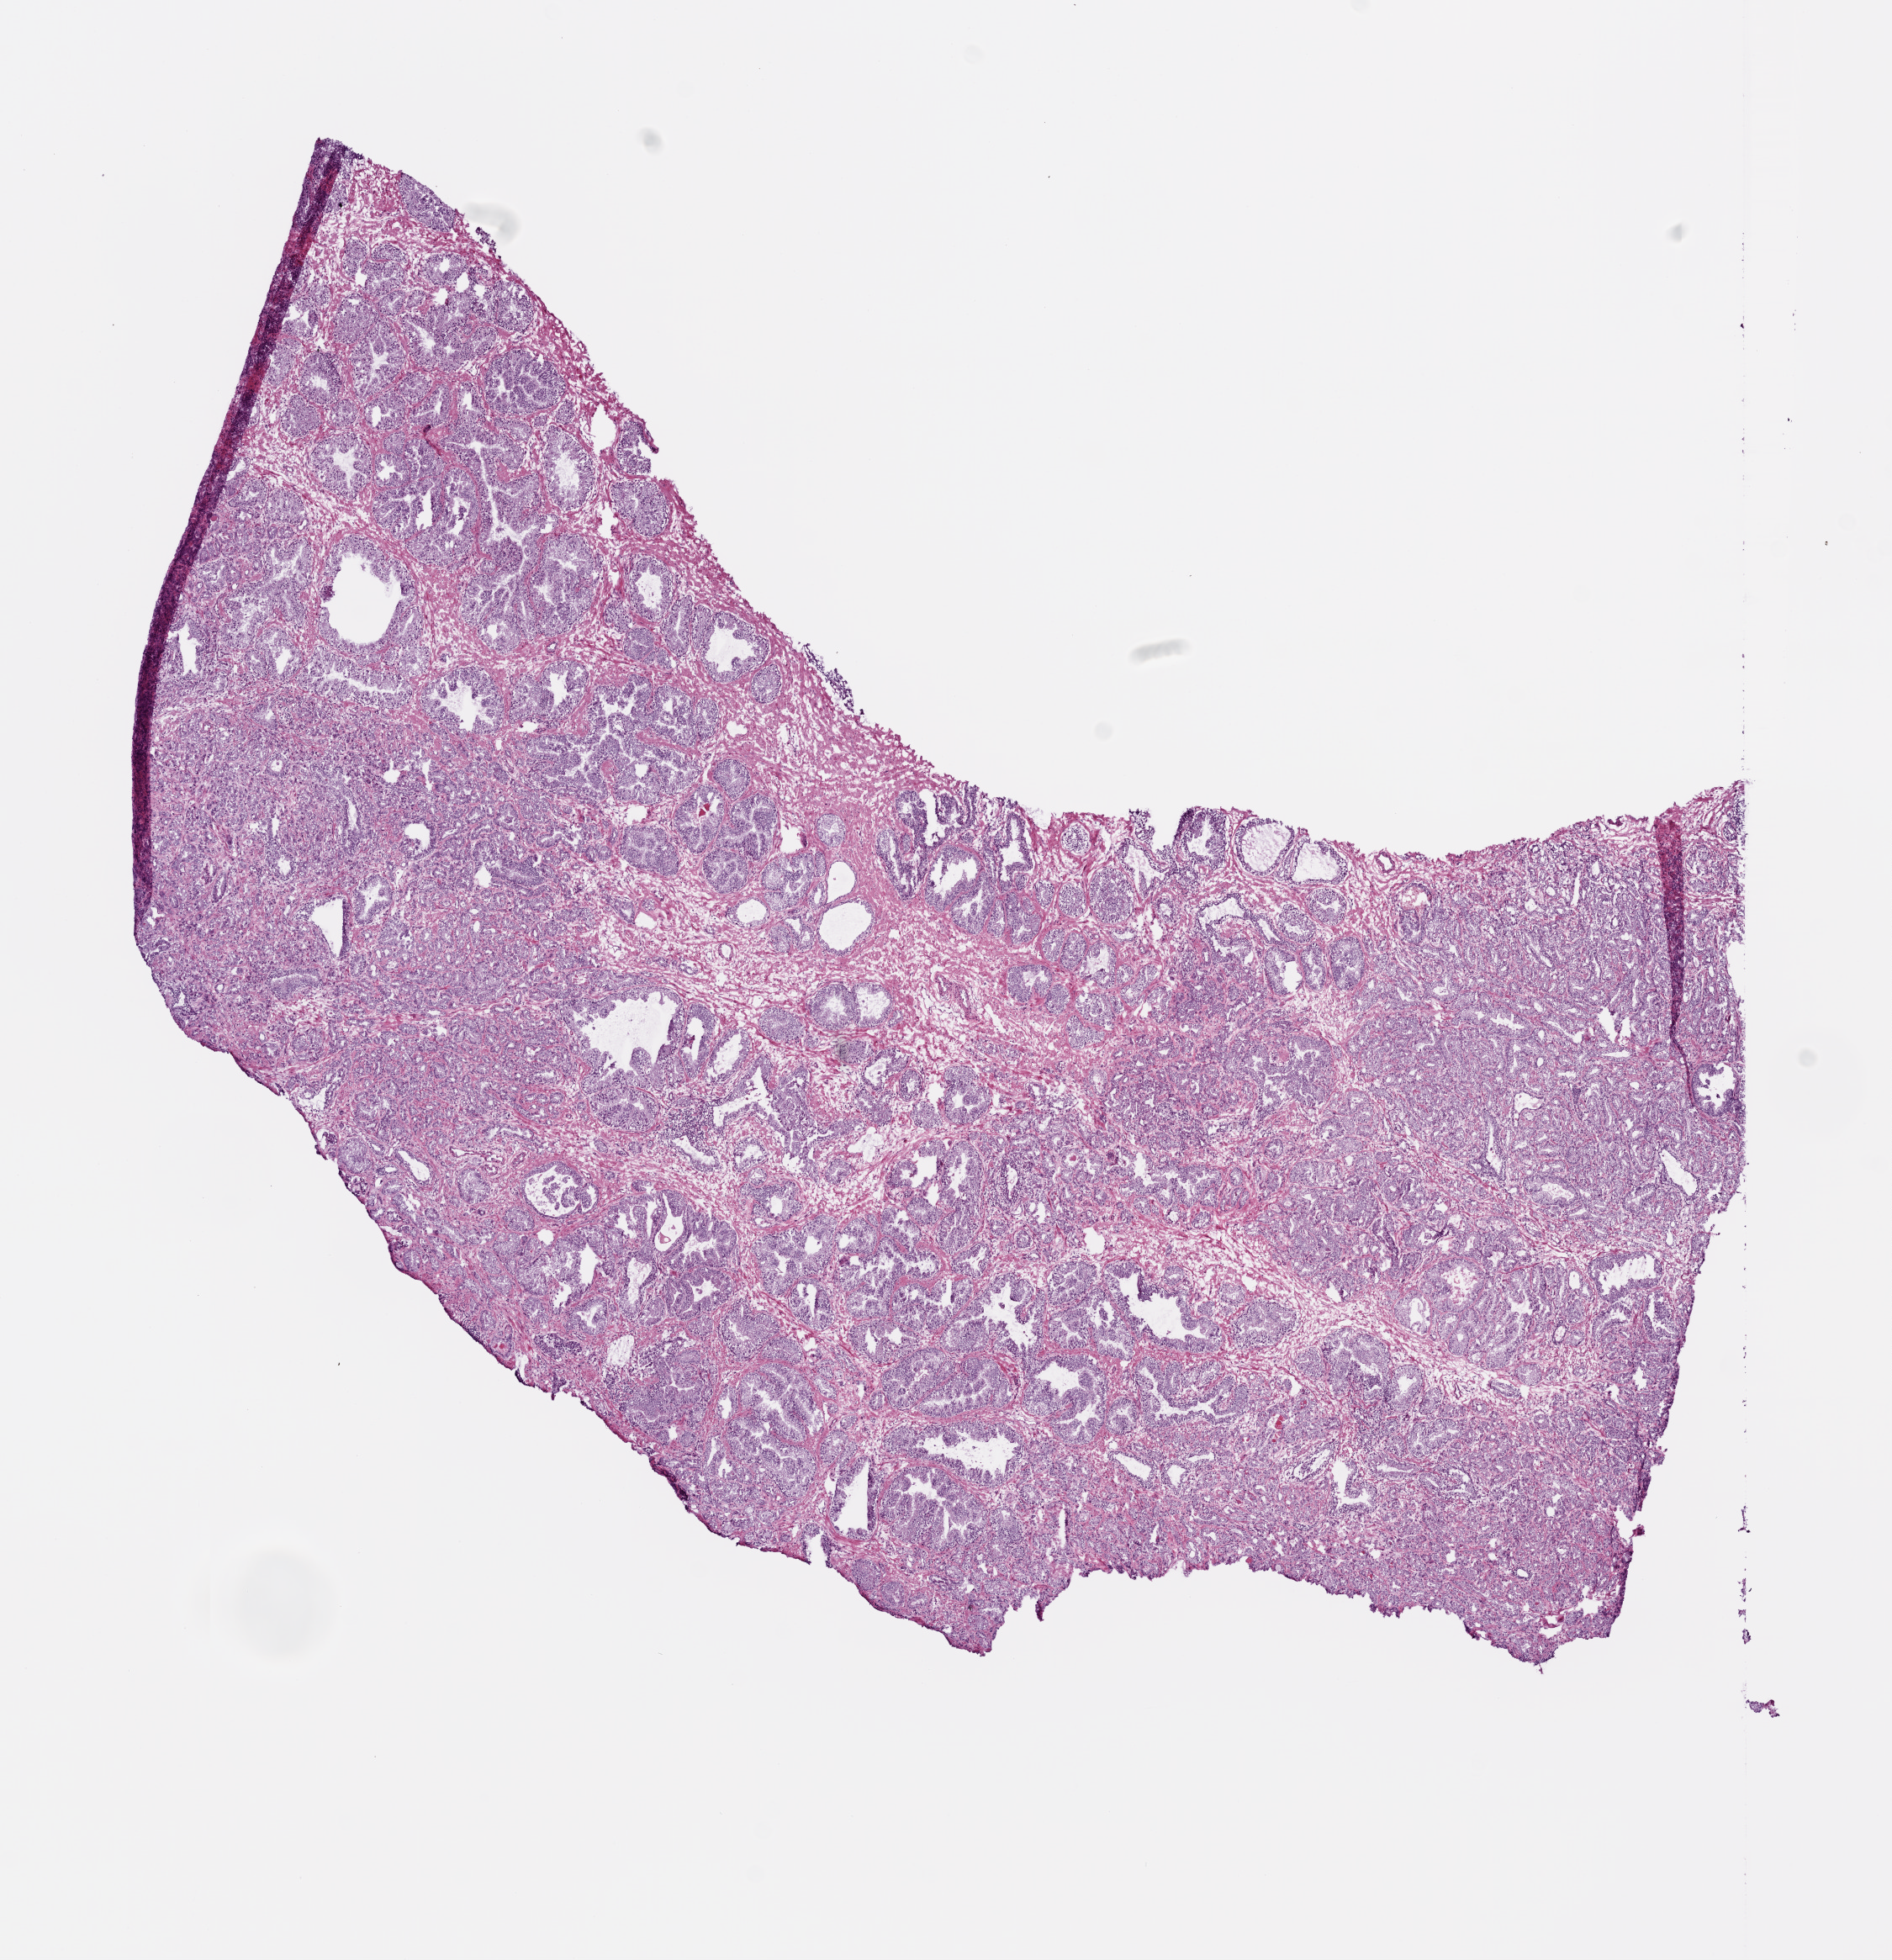
Whole-slide histology image, H&E — whole scanned area (about 9.0 x 9.4 mm) shown as a low-resolution overview, frozen section from the bottom of the tissue portion, prostate, primary tumour sample. Male, age 64 years at initial diagnosis. Gleason score: 7 (4+3). Pathologist review of this section (percent, as recorded): tumour cells 55%, tumour nuclei 60%, normal cells 30%, stromal cells 15%, necrosis 0%. Inflammatory infiltration, as recorded: lymphocyte infiltration 0%, monocyte infiltration 0%, neutrophil infiltration 0%.
Lymph nodes positive (case pathology): 0 of 2 examined. Diagnosis: Acinar cell carcinoma.